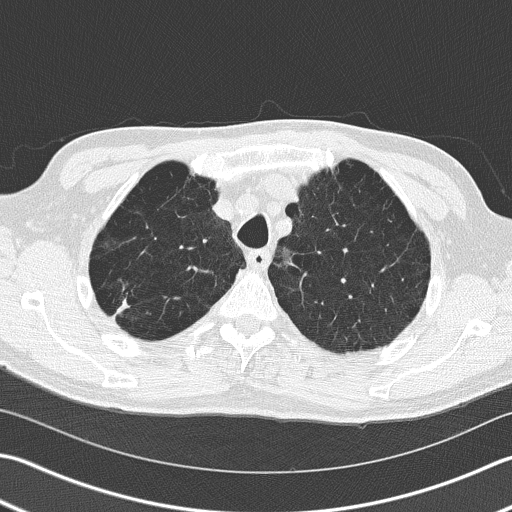
Axial slice from a low-dose chest CT screening exam. Baseline annual screen. Lung window (W 1500 / L -600 HU). 2 mm slice thickness. Lung (sharp) reconstruction kernel (B50f). 512 × 512 image matrix, field of view 346 × 346 mm. Male participant, aged 66 years at enrolment. Current smoker at enrolment.
Lesion marked by an expert reader, bounding box [x1, y1, x2, y2] px = [96, 281, 150, 340]. Reader record for this screening exam (exam-level; its link to the box is not recorded): non-calcified nodule or mass ≥4 mm, right upper lobe, 39 × 23 mm, spiculated (stellate) margins, soft tissue attenuation. Lung cancer was diagnosed 36 days after this screen: squamous cell carcinoma, NOS, right upper lobe, poorly differentiated (G3), stage IB (AJCC 6th edition), 23 mm at pathology.